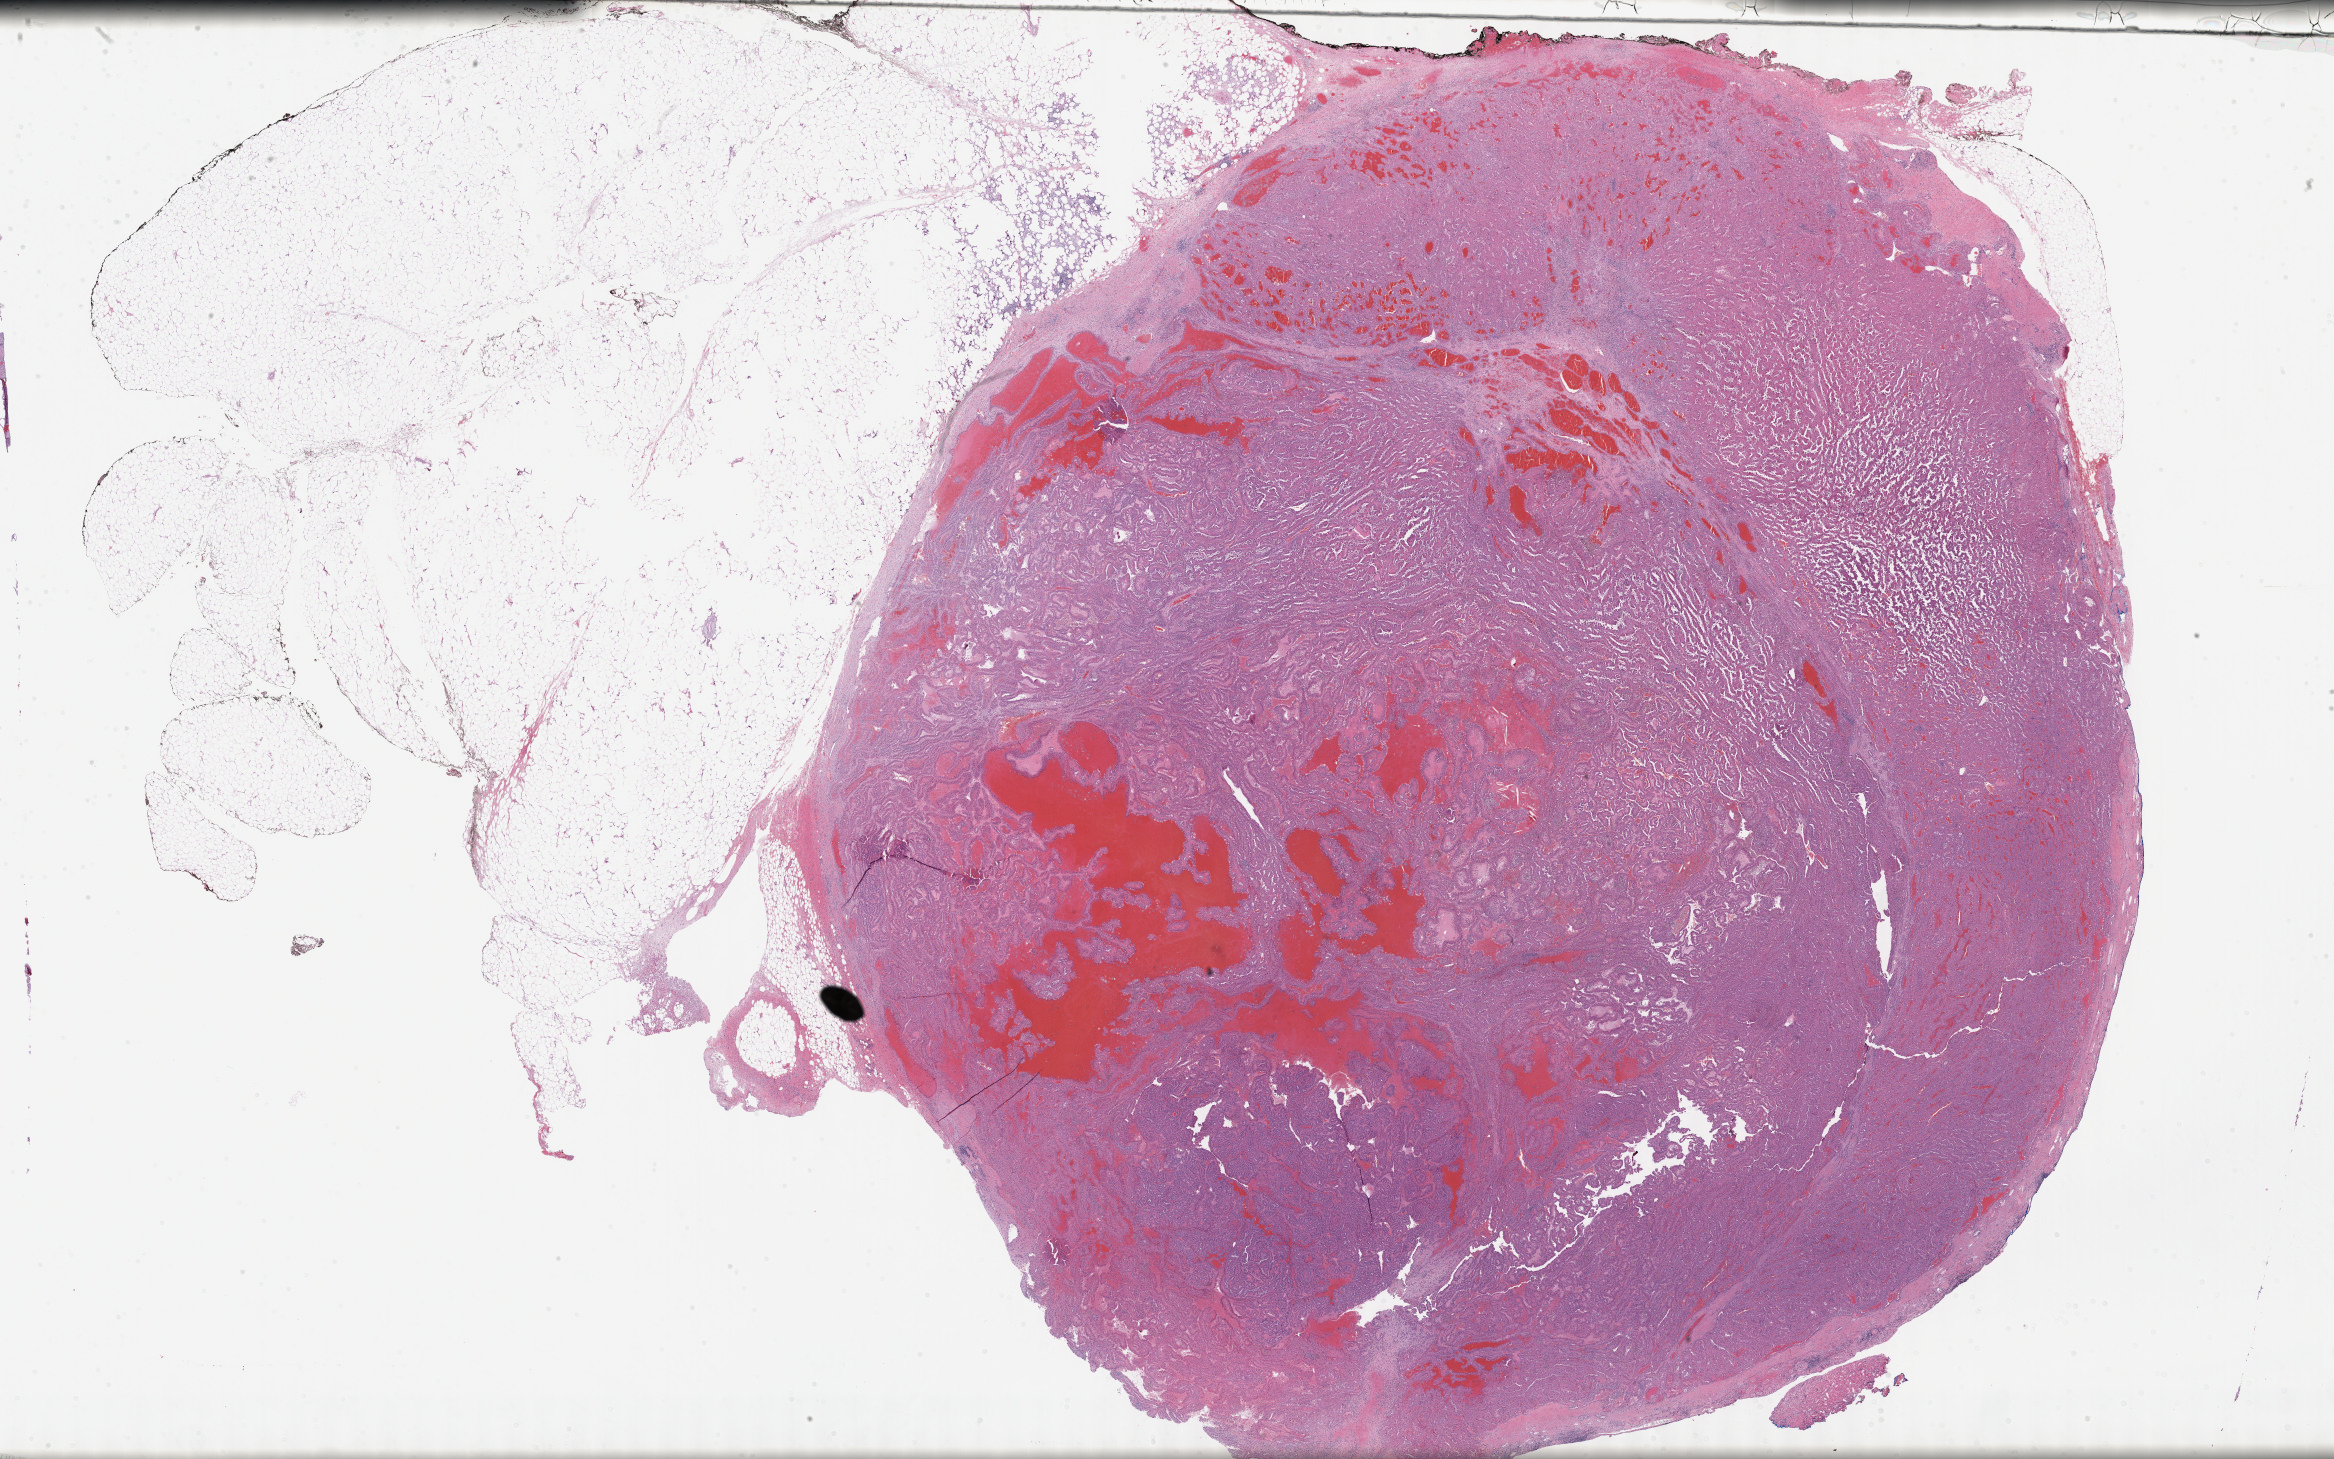
Whole-slide histology image, H&E-stained — whole scanned area (about 37.8 x 23.6 mm, acquisition: 40x scan) shown as a low-resolution overview. Formalin-fixed paraffin-embedded (FFPE) diagnostic section. Primary tumour sample from the kidney. Male patient; age at initial diagnosis 62 years.
Diagnosis: Papillary adenocarcinoma, NOS. AJCC pathologic stage: I (7th edition).